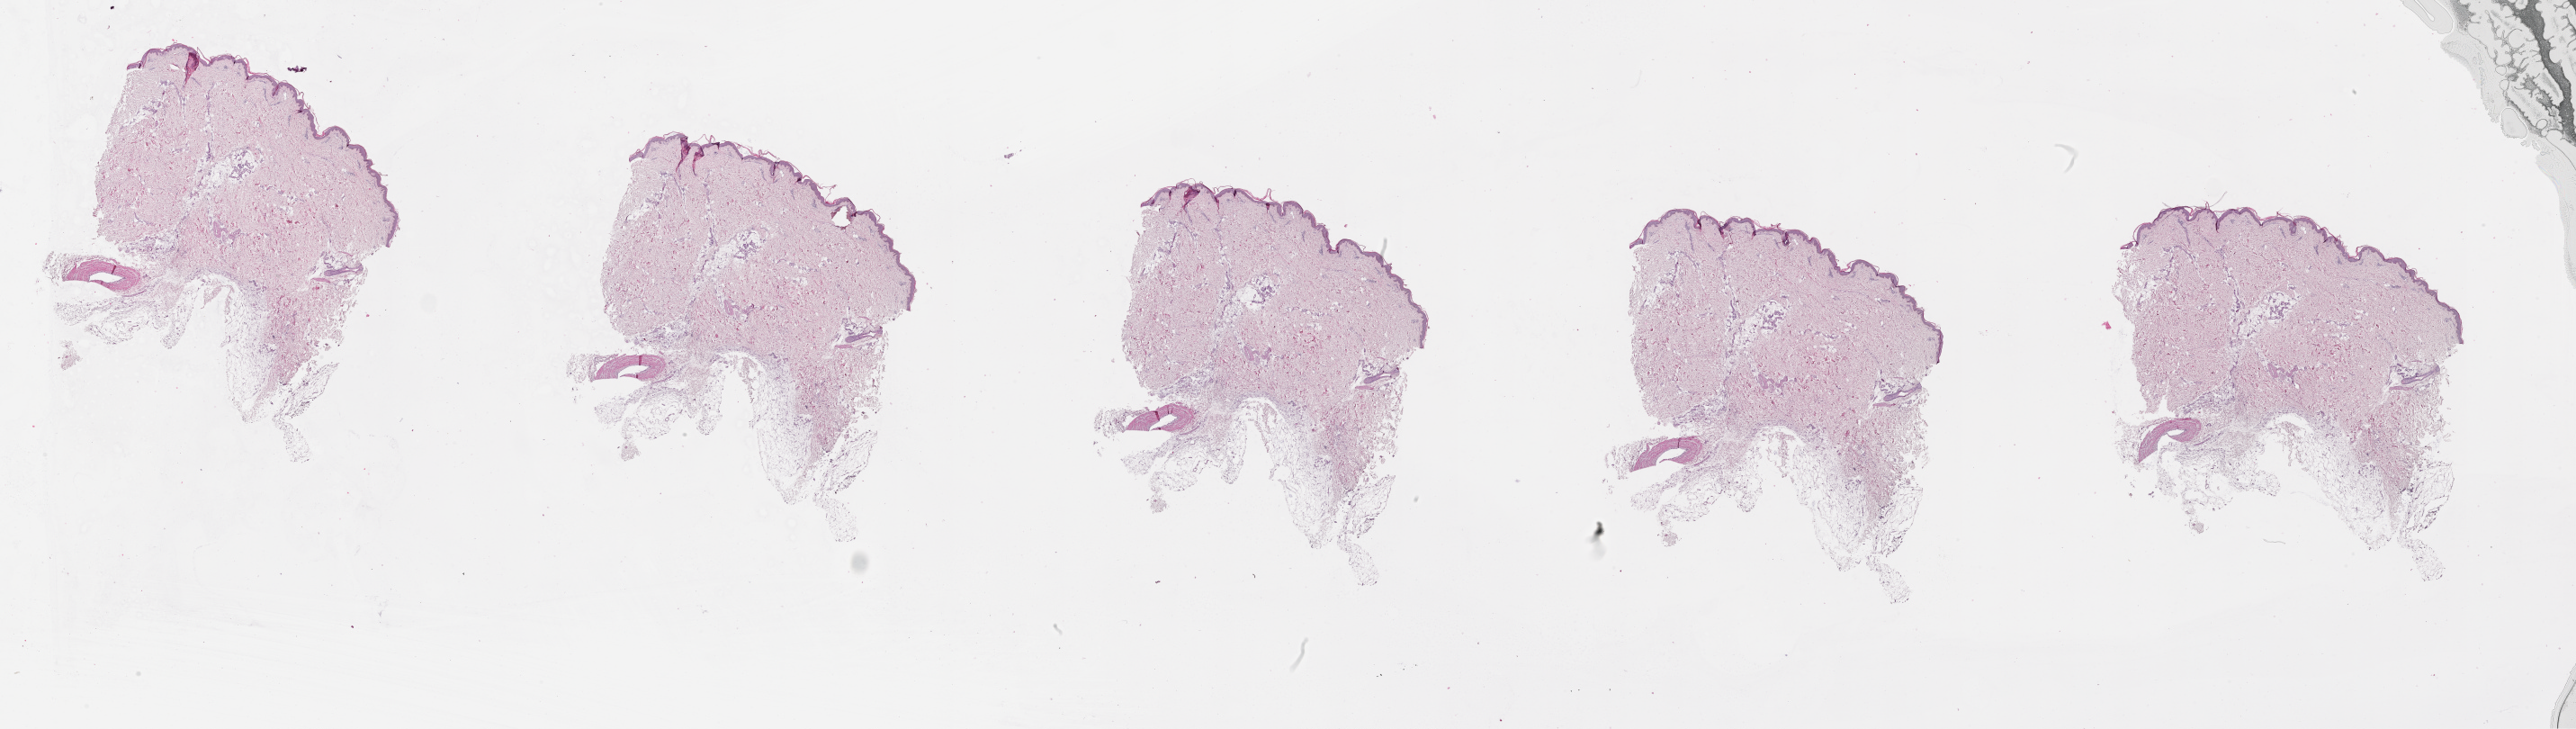
Whole-slide histology image, Hematoxylin and eosin (H&E) stained, whole scanned area (about 46.1 x 13.0 mm, acquisition: 20x scan) shown as a low-resolution overview. Female, 70 y/o.
Patient diagnosis: Malignant melanoma, NOS.